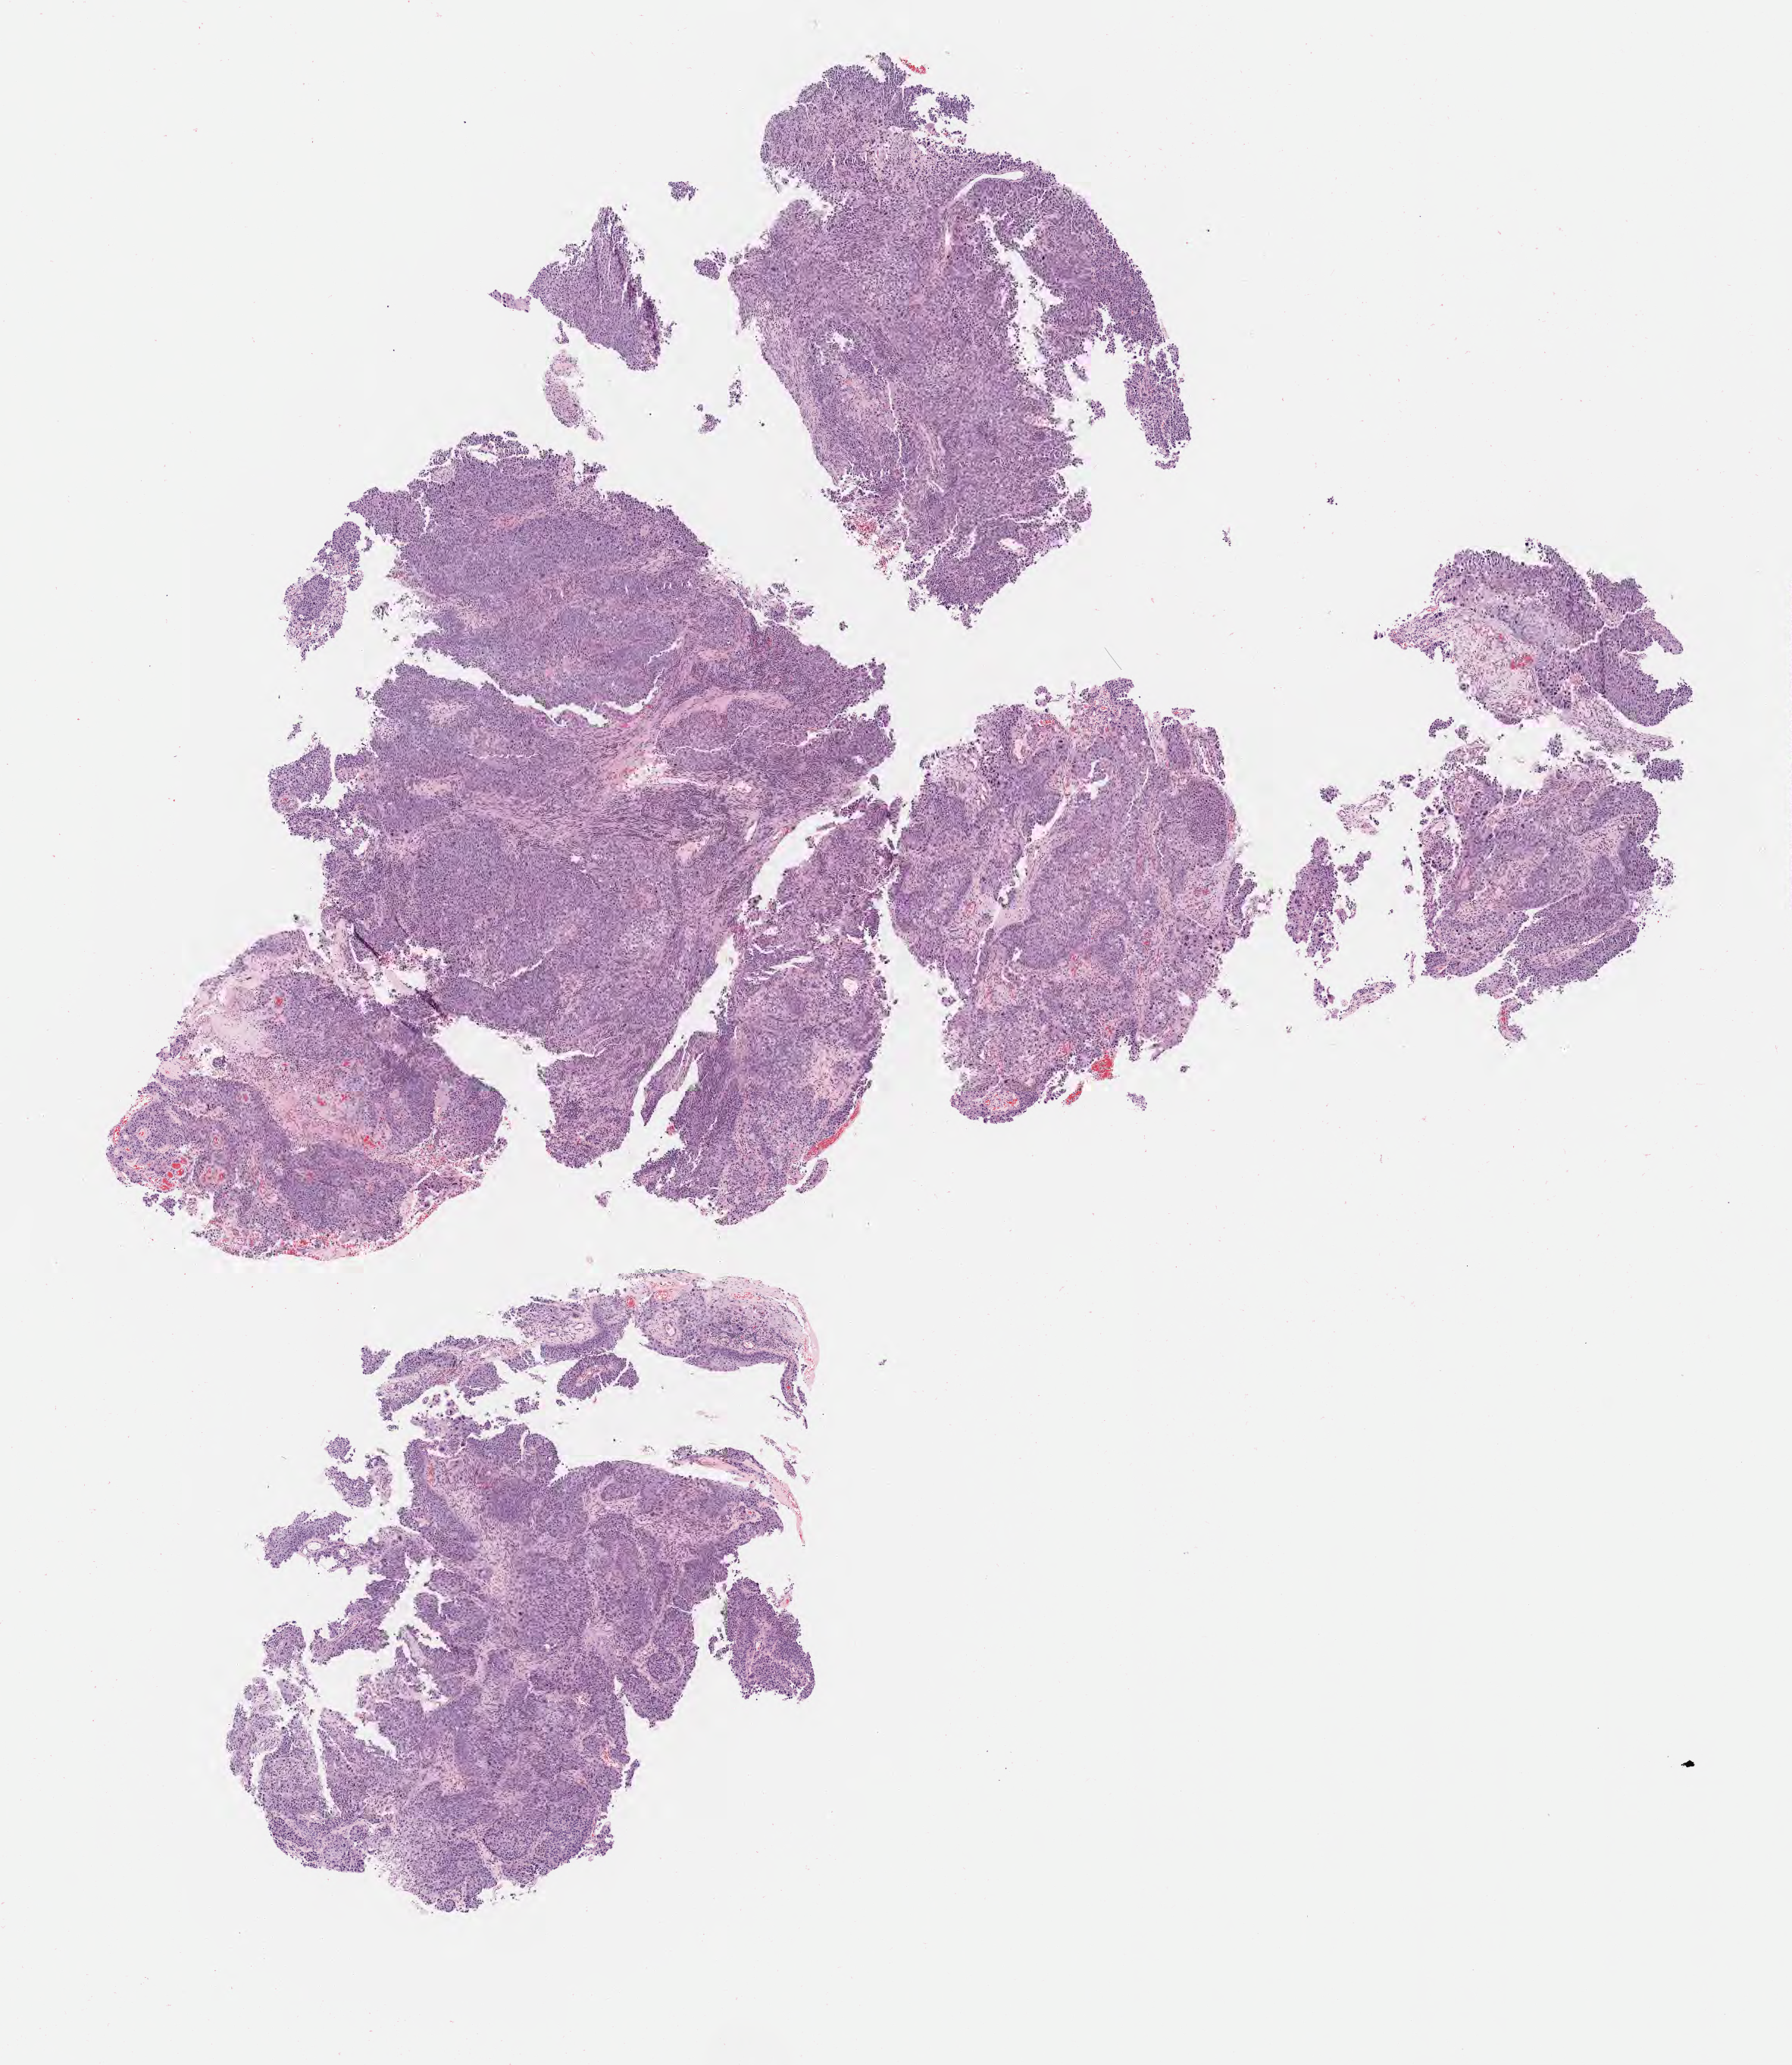
Haematoxylin and eosin whole-slide image — a low-resolution overview of the entire scanned area, about 9.6 x 11.0 mm; specimen: tumor tissue; site: cervix. Female patient, age 59 years.
Diagnosis: Squamous cell carcinoma, large cell, nonkeratinizing, NOS.